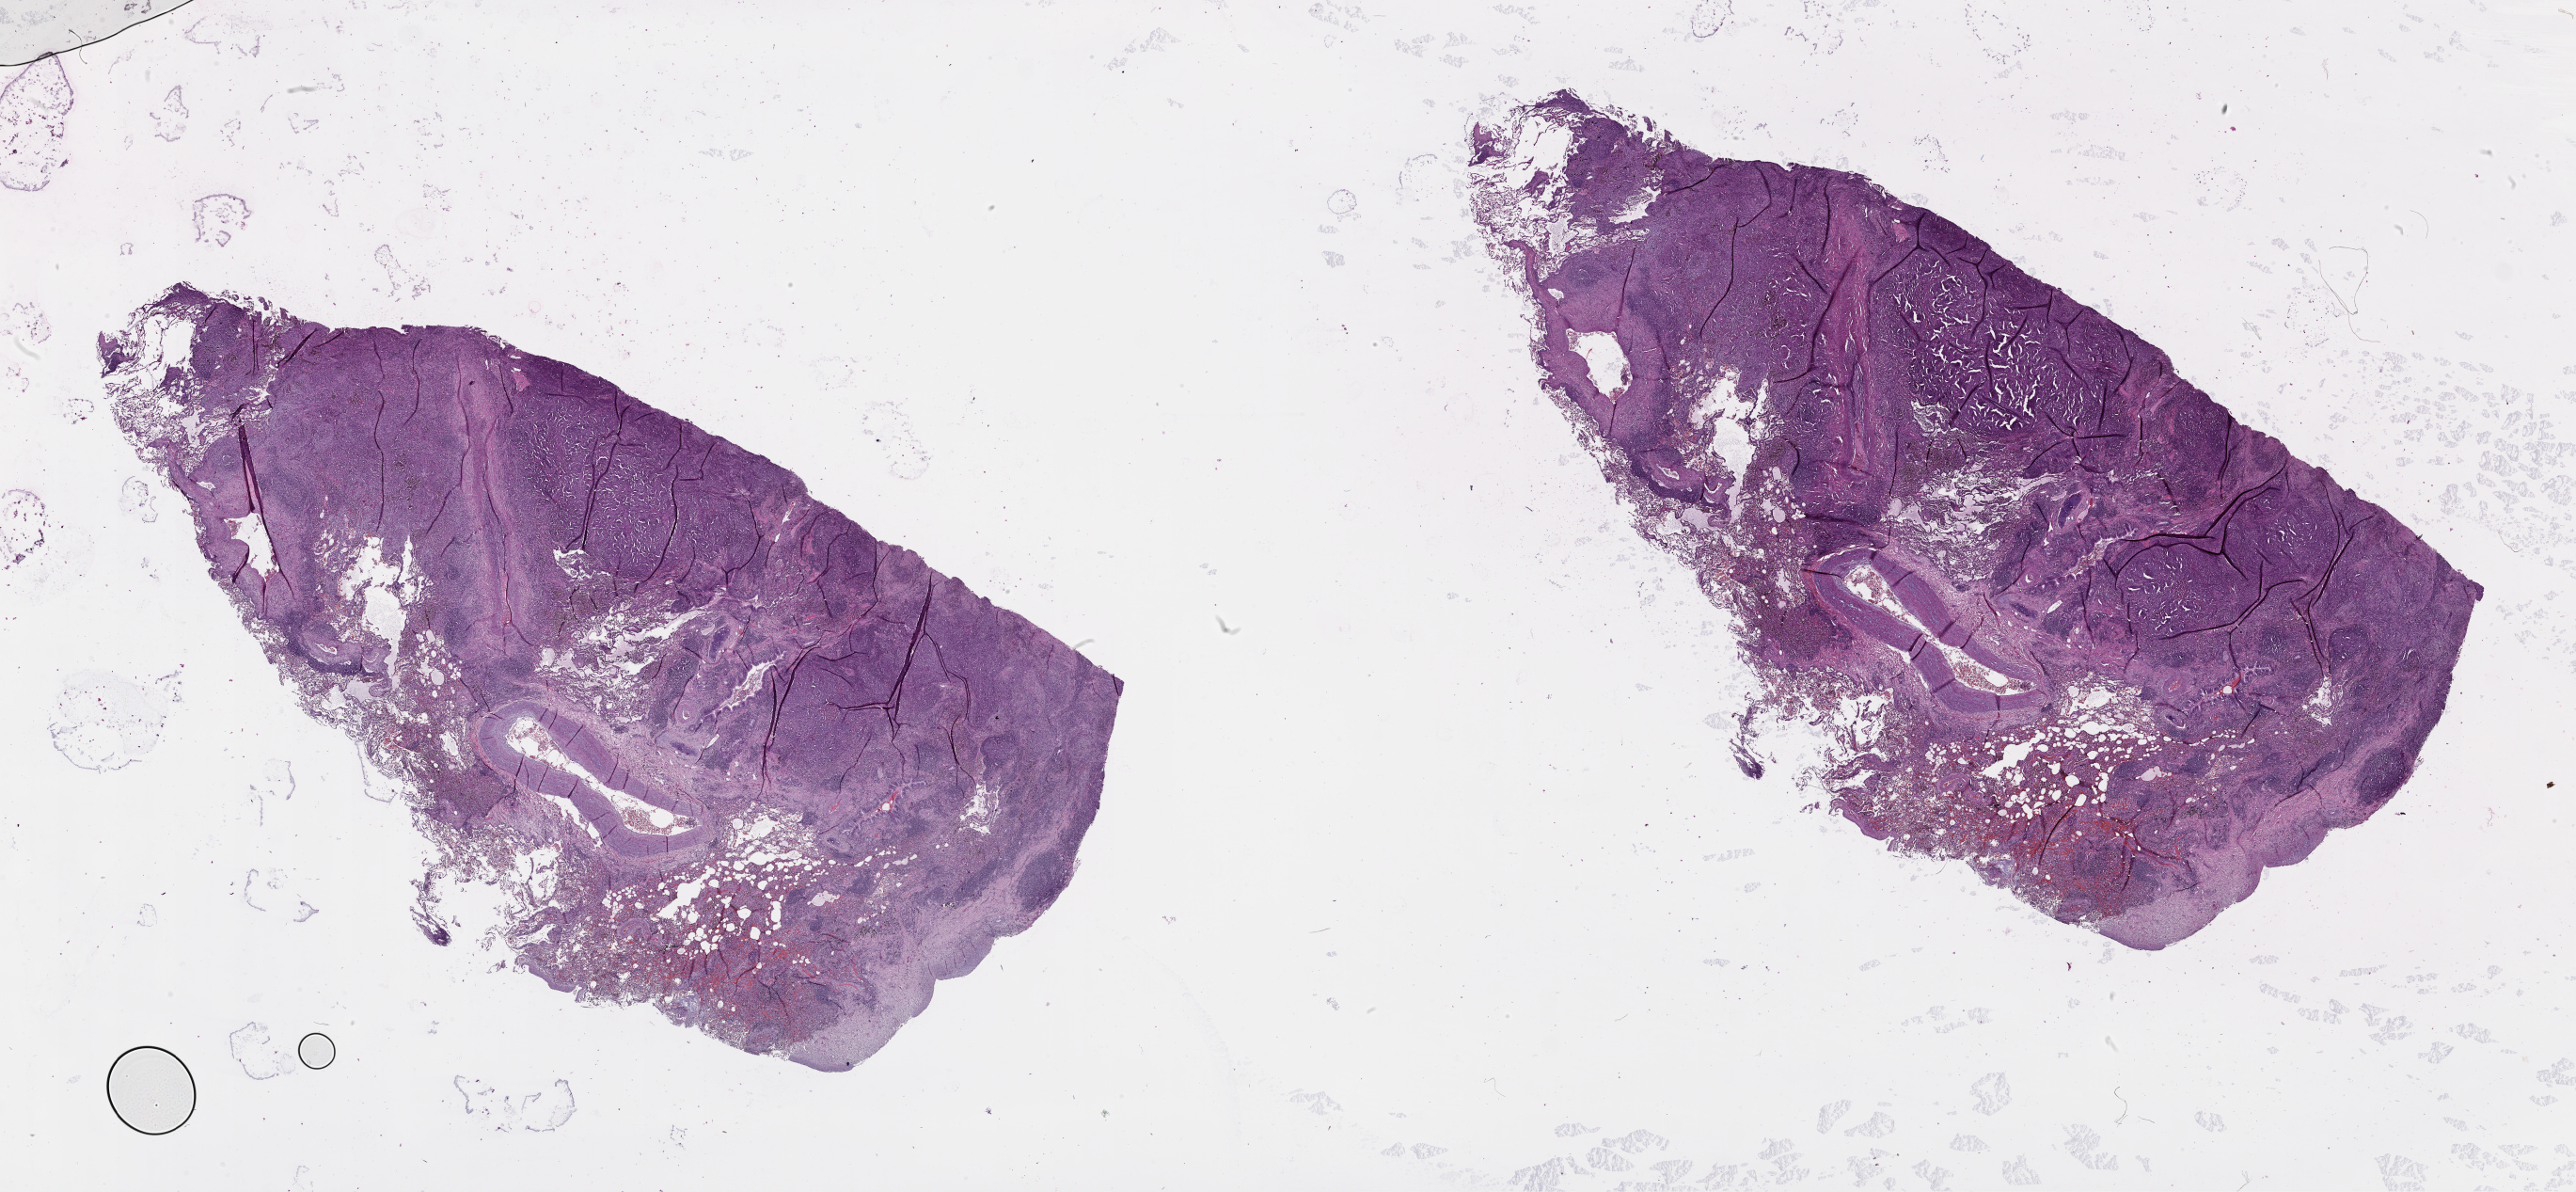
Digitized H&E-stained tissue section (whole slide) — low-resolution overview of the scanned area, about 44.1 x 20.4 mm (acquisition: 20x scan); lung, tumour tissue. Male, 65 y/o.
- patient diagnosis (cohort enrolment): squamous cell carcinoma (lung)